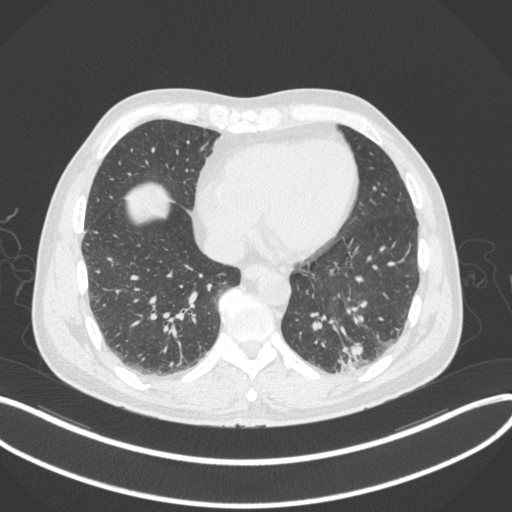
Chest CT, one axial slice; position 90 of 313 along the scan axis; reconstruction kernel B31f; 120 kVp; lung window (W 1500 / L -600 HU); 1 mm slice thickness; 512 × 512 image matrix, field of view 400 × 400 mm. Male patient, age 54 years. From the clinical record (not read from this slice): clinical TNM (as recorded): T1c N0 M1; histopathological grade: G3.
Structures marked on this image (rectangle marked by the reading radiologist):
- lung tumour (recorded histology: adenocarcinoma): bounding box (x1, y1, x2, y2) in pixels: (332, 342, 364, 371)